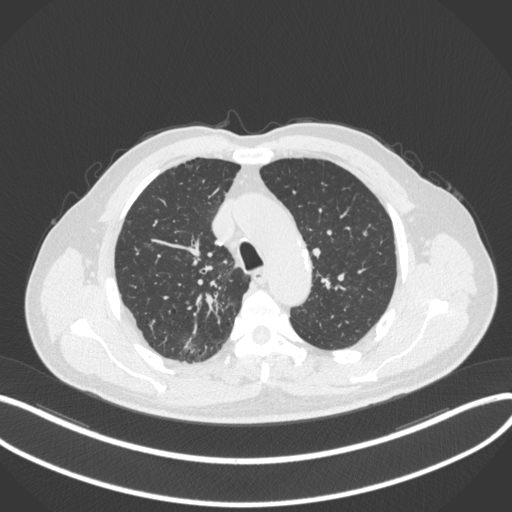
Chest CT, one axial slice; position 277 of 366 along the scan axis; 120 kVp; lung window (W 1500 / L -600 HU); 1 mm slice thickness; 512 × 512 image matrix, field of view 400 × 400 mm. Male patient, age 69 years. From the clinical record (not read from this slice): clinical TNM (as recorded): T1b N0 M0; histopathological grade: G2-3.
Structures marked on this image (rectangle marked by the reading radiologist):
- lung tumour (recorded histology: adenocarcinoma): box from (x=182, y=337) to (x=204, y=360) px